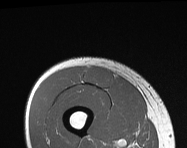
MRI of an extremity soft-tissue mass, one axial slice. Slice 41 of 114 in the series (ordered by position). MR volume resampled by the dataset authors to the PET/CT grid (not the native acquisition matrix). 187 × 148 image matrix. Male patient. Case-level facts recorded for this patient, not image findings: histological type: pleiomorphic leiomyosarcoma; grade: intermediate; site of the primary tumour: right thigh.
Outlined on this slice (expert contour drawn on MRI and transferred to this co-registered scan by the dataset authors):
- gross tumour volume including surrounding oedema: bounding box <84,68,112,87> (left, top, right, bottom; pixels)